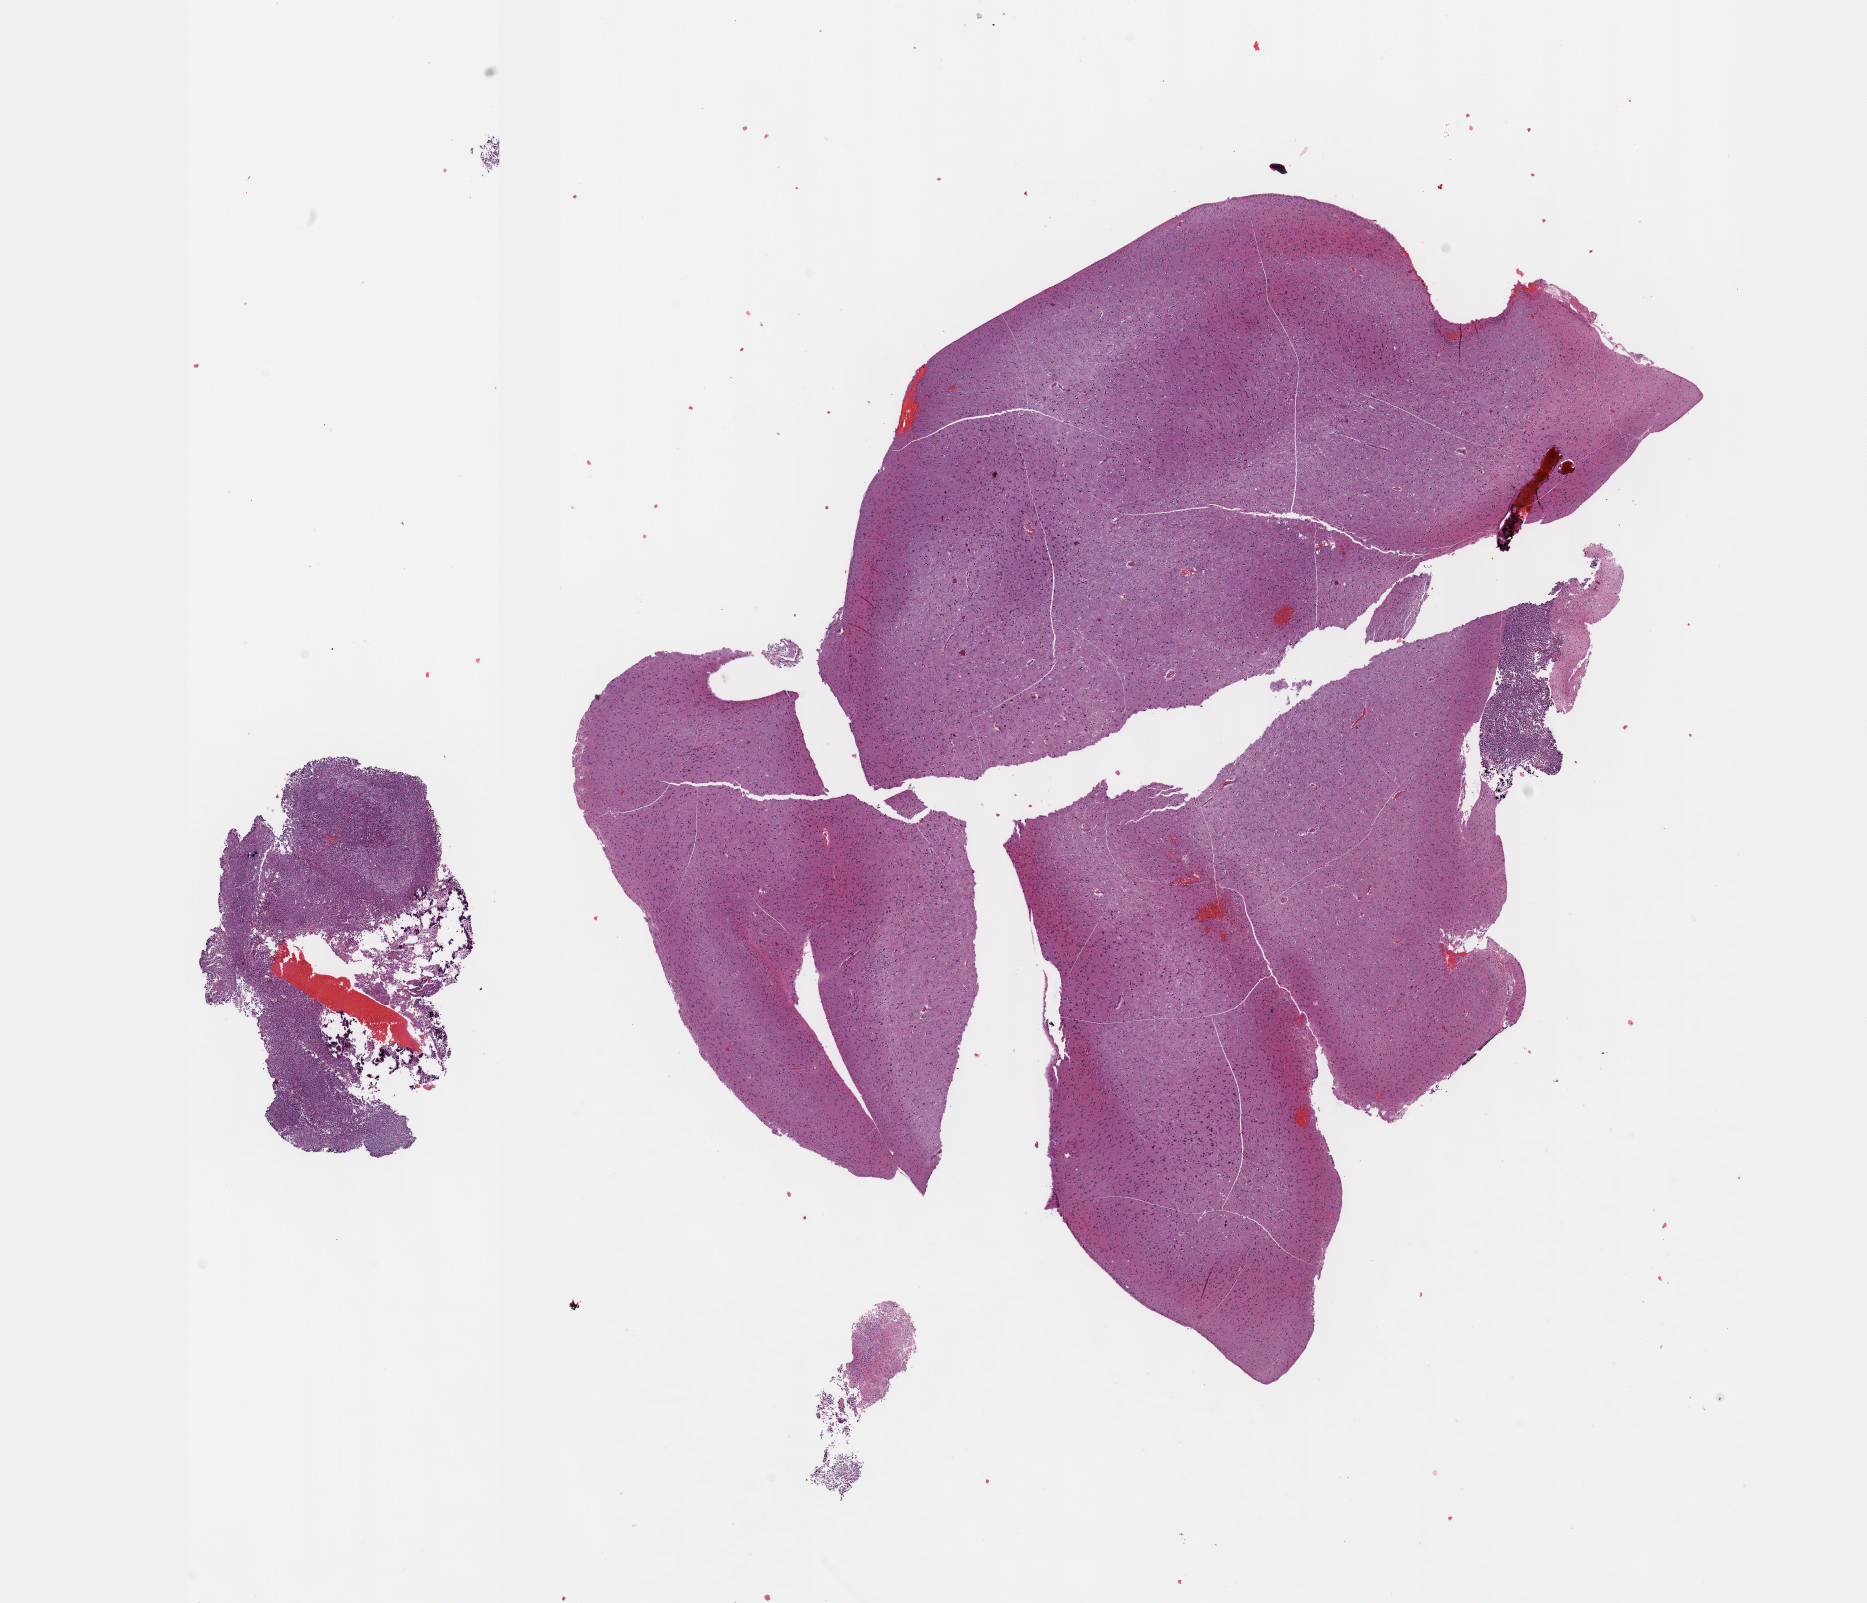
Whole-slide histology image, H&E, whole scanned area (about 15.1 x 13.0 mm, acquisition: 40x scan) shown as a low-resolution overview, FFPE section, brain, primary tumour sample. Male, age 74 years at initial diagnosis. Histologic grade: G3 (poorly differentiated).
Histologic diagnosis: Oligodendroglioma, anaplastic (cerebrum).